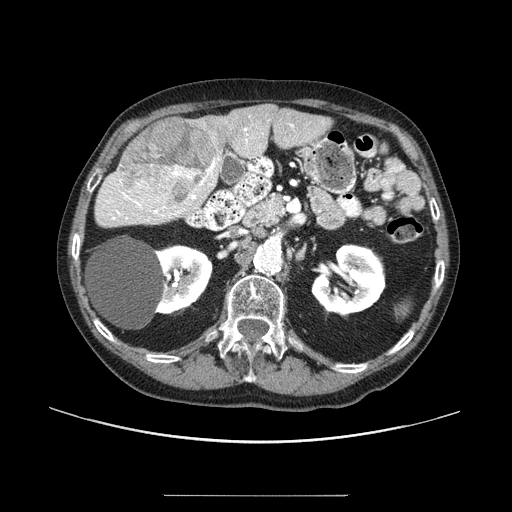
Contrast-enhanced abdominal CT (liver protocol), one axial slice; slice 42 of 91 in the series (ordered by position); reconstruction kernel STANDARD; 100 kVp; one of 2 acquisitions stored at this slice position; soft-tissue window (W 400 / L 40 HU); 2.5 mm slice thickness; 512 × 512 image matrix. From the clinical record (not read from this slice): diagnosis: hepatocellular carcinoma (patient treated with transarterial chemoembolisation; whether this scan precedes or follows treatment is not stated here); TNM stage (as recorded): Stage-I; Child-Pugh class: A; tumour differentiation: moderately differentiated.
Structures marked on this image (semi-automatic segmentation, software-assisted and operator-edited):
- liver parenchyma outside the tumour (the mass and vessels are separate outlines, so this box may not span the whole liver): bounding box <124,104,332,222> (left, top, right, bottom; pixels)
- mass: <120,118,216,208>
- liver vessels: <133,124,294,211>